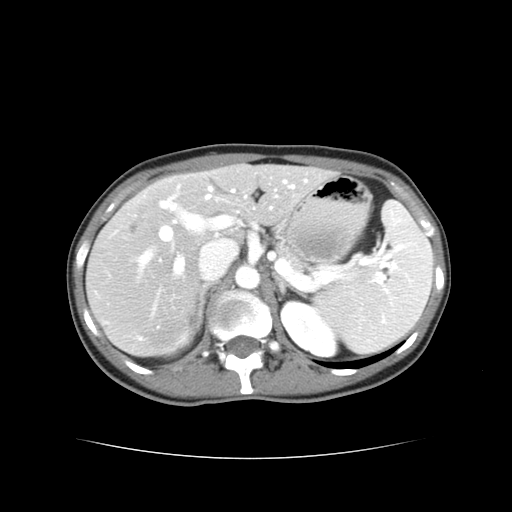
Contrast-enhanced abdominal CT, one axial slice; slice 24 of 38 in the series (ordered by position); reconstruction kernel STANDARD; 120 kVp; intravenous contrast given; soft-tissue window (W 400 / L 40 HU); 512 × 512 image matrix. Female patient, age 54 years. From the clinical record (not read from this slice): diagnosis: colorectal cancer liver metastases, imaged before liver resection; multiple liver metastases: yes; largest metastasis: 1.1 cm.
Structures marked on this image (expert manual segmentation):
- hepatic veins: bounding box (x1, y1, x2, y2) in pixels: (142, 186, 294, 268)
- liver: (88, 165, 328, 354)
- planned liver remnant (the part of the liver to remain after resection): (214, 165, 328, 223)
- portal vein (with intrahepatic branches): (140, 180, 307, 272)
- liver metastasis: (133, 218, 143, 230)